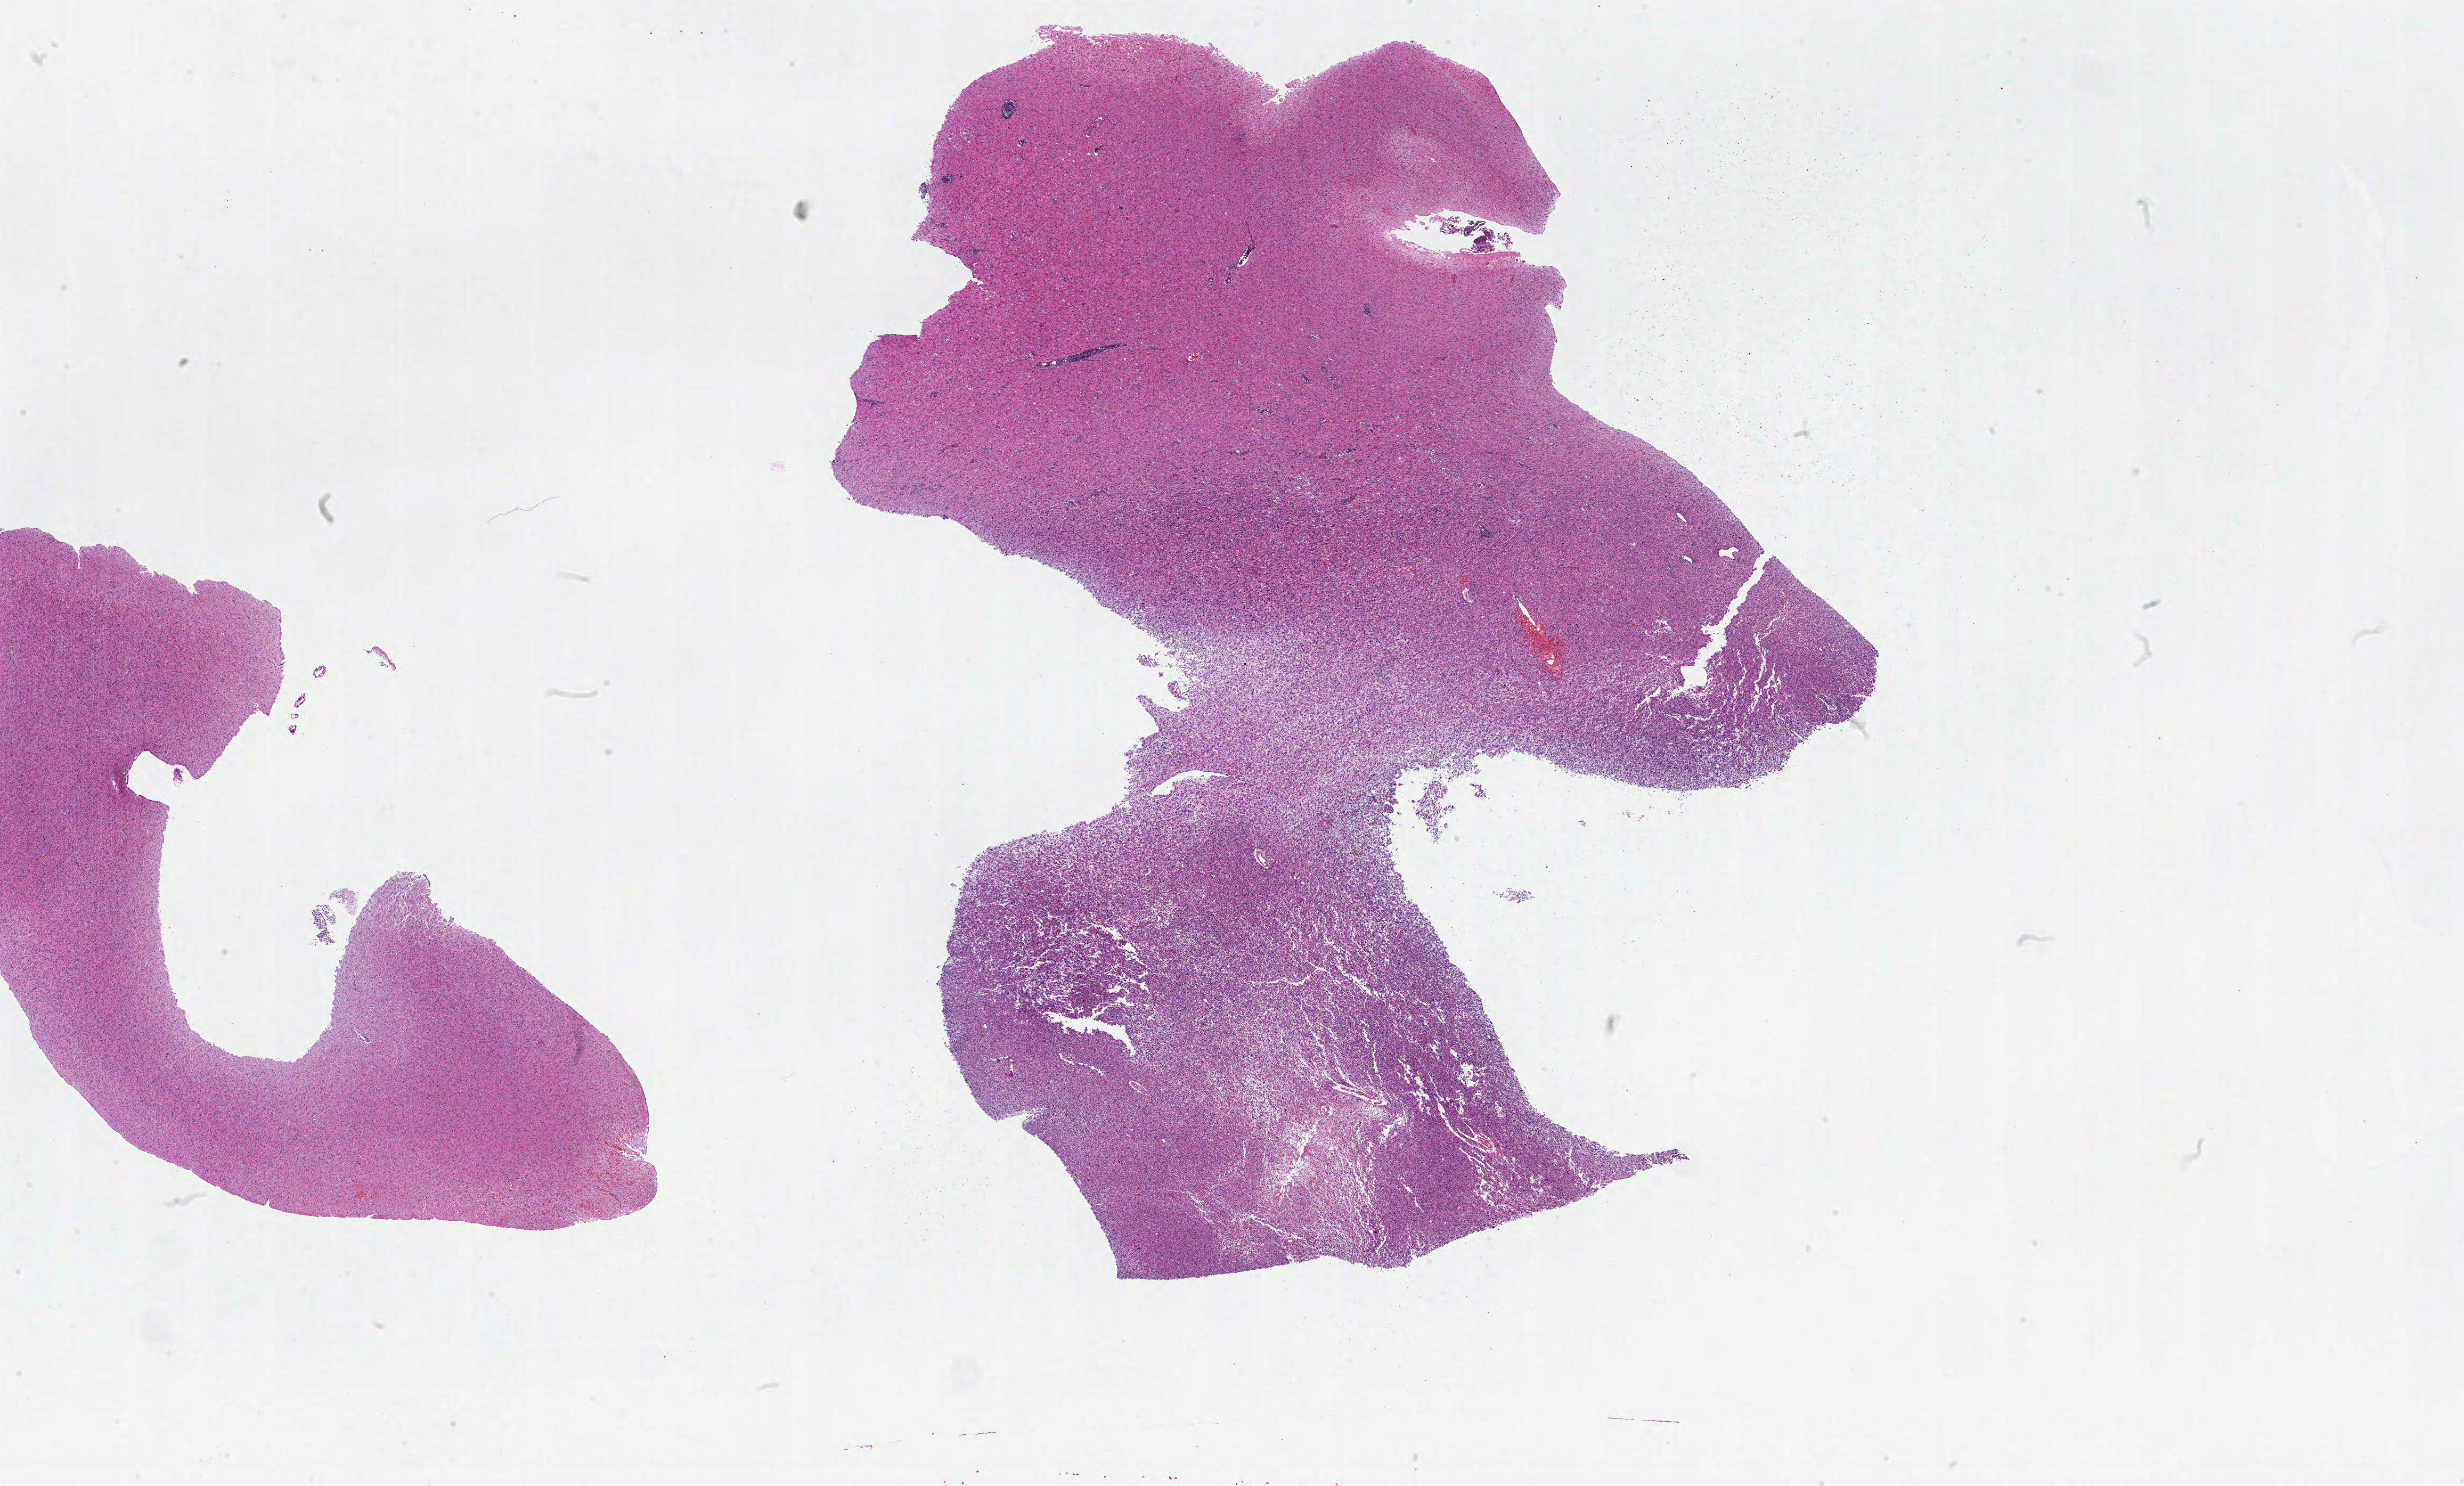
Whole-slide histology image, H&E — a low-resolution overview of the entire scanned area, about 37.0 x 22.3 mm (from a 20x scan); FFPE section; sample: primary tumour, brain. Male patient; age at initial diagnosis 63 years.
Histologic diagnosis: Glioblastoma.